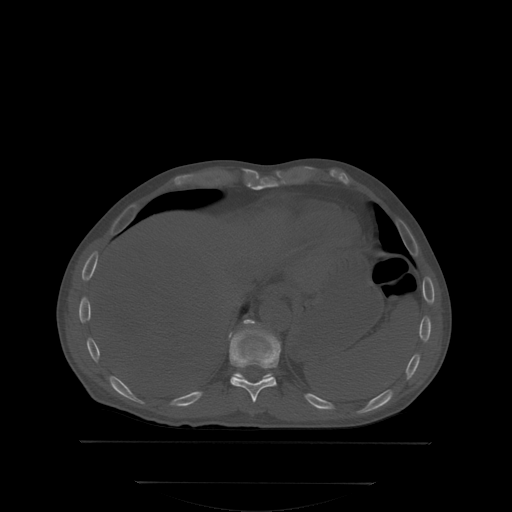
CT including the spine, one axial slice. Position 191 of 350 along the scan axis. Bone window (W 1800 / L 400 HU). 512 × 512 image matrix, field of view 500 × 500 mm. Patient: male, 58 years. From the clinical record (not read from this slice): primary cancer: prostate; vertebrae with lytic lesions (as recorded): L1.
Annotated regions visible in this slice (semi-automatically segmented with operator editing):
- T10 vertebra: box from (x=230, y=325) to (x=279, y=402) px
- T11 vertebra: (x=236, y=373)–(x=269, y=379)